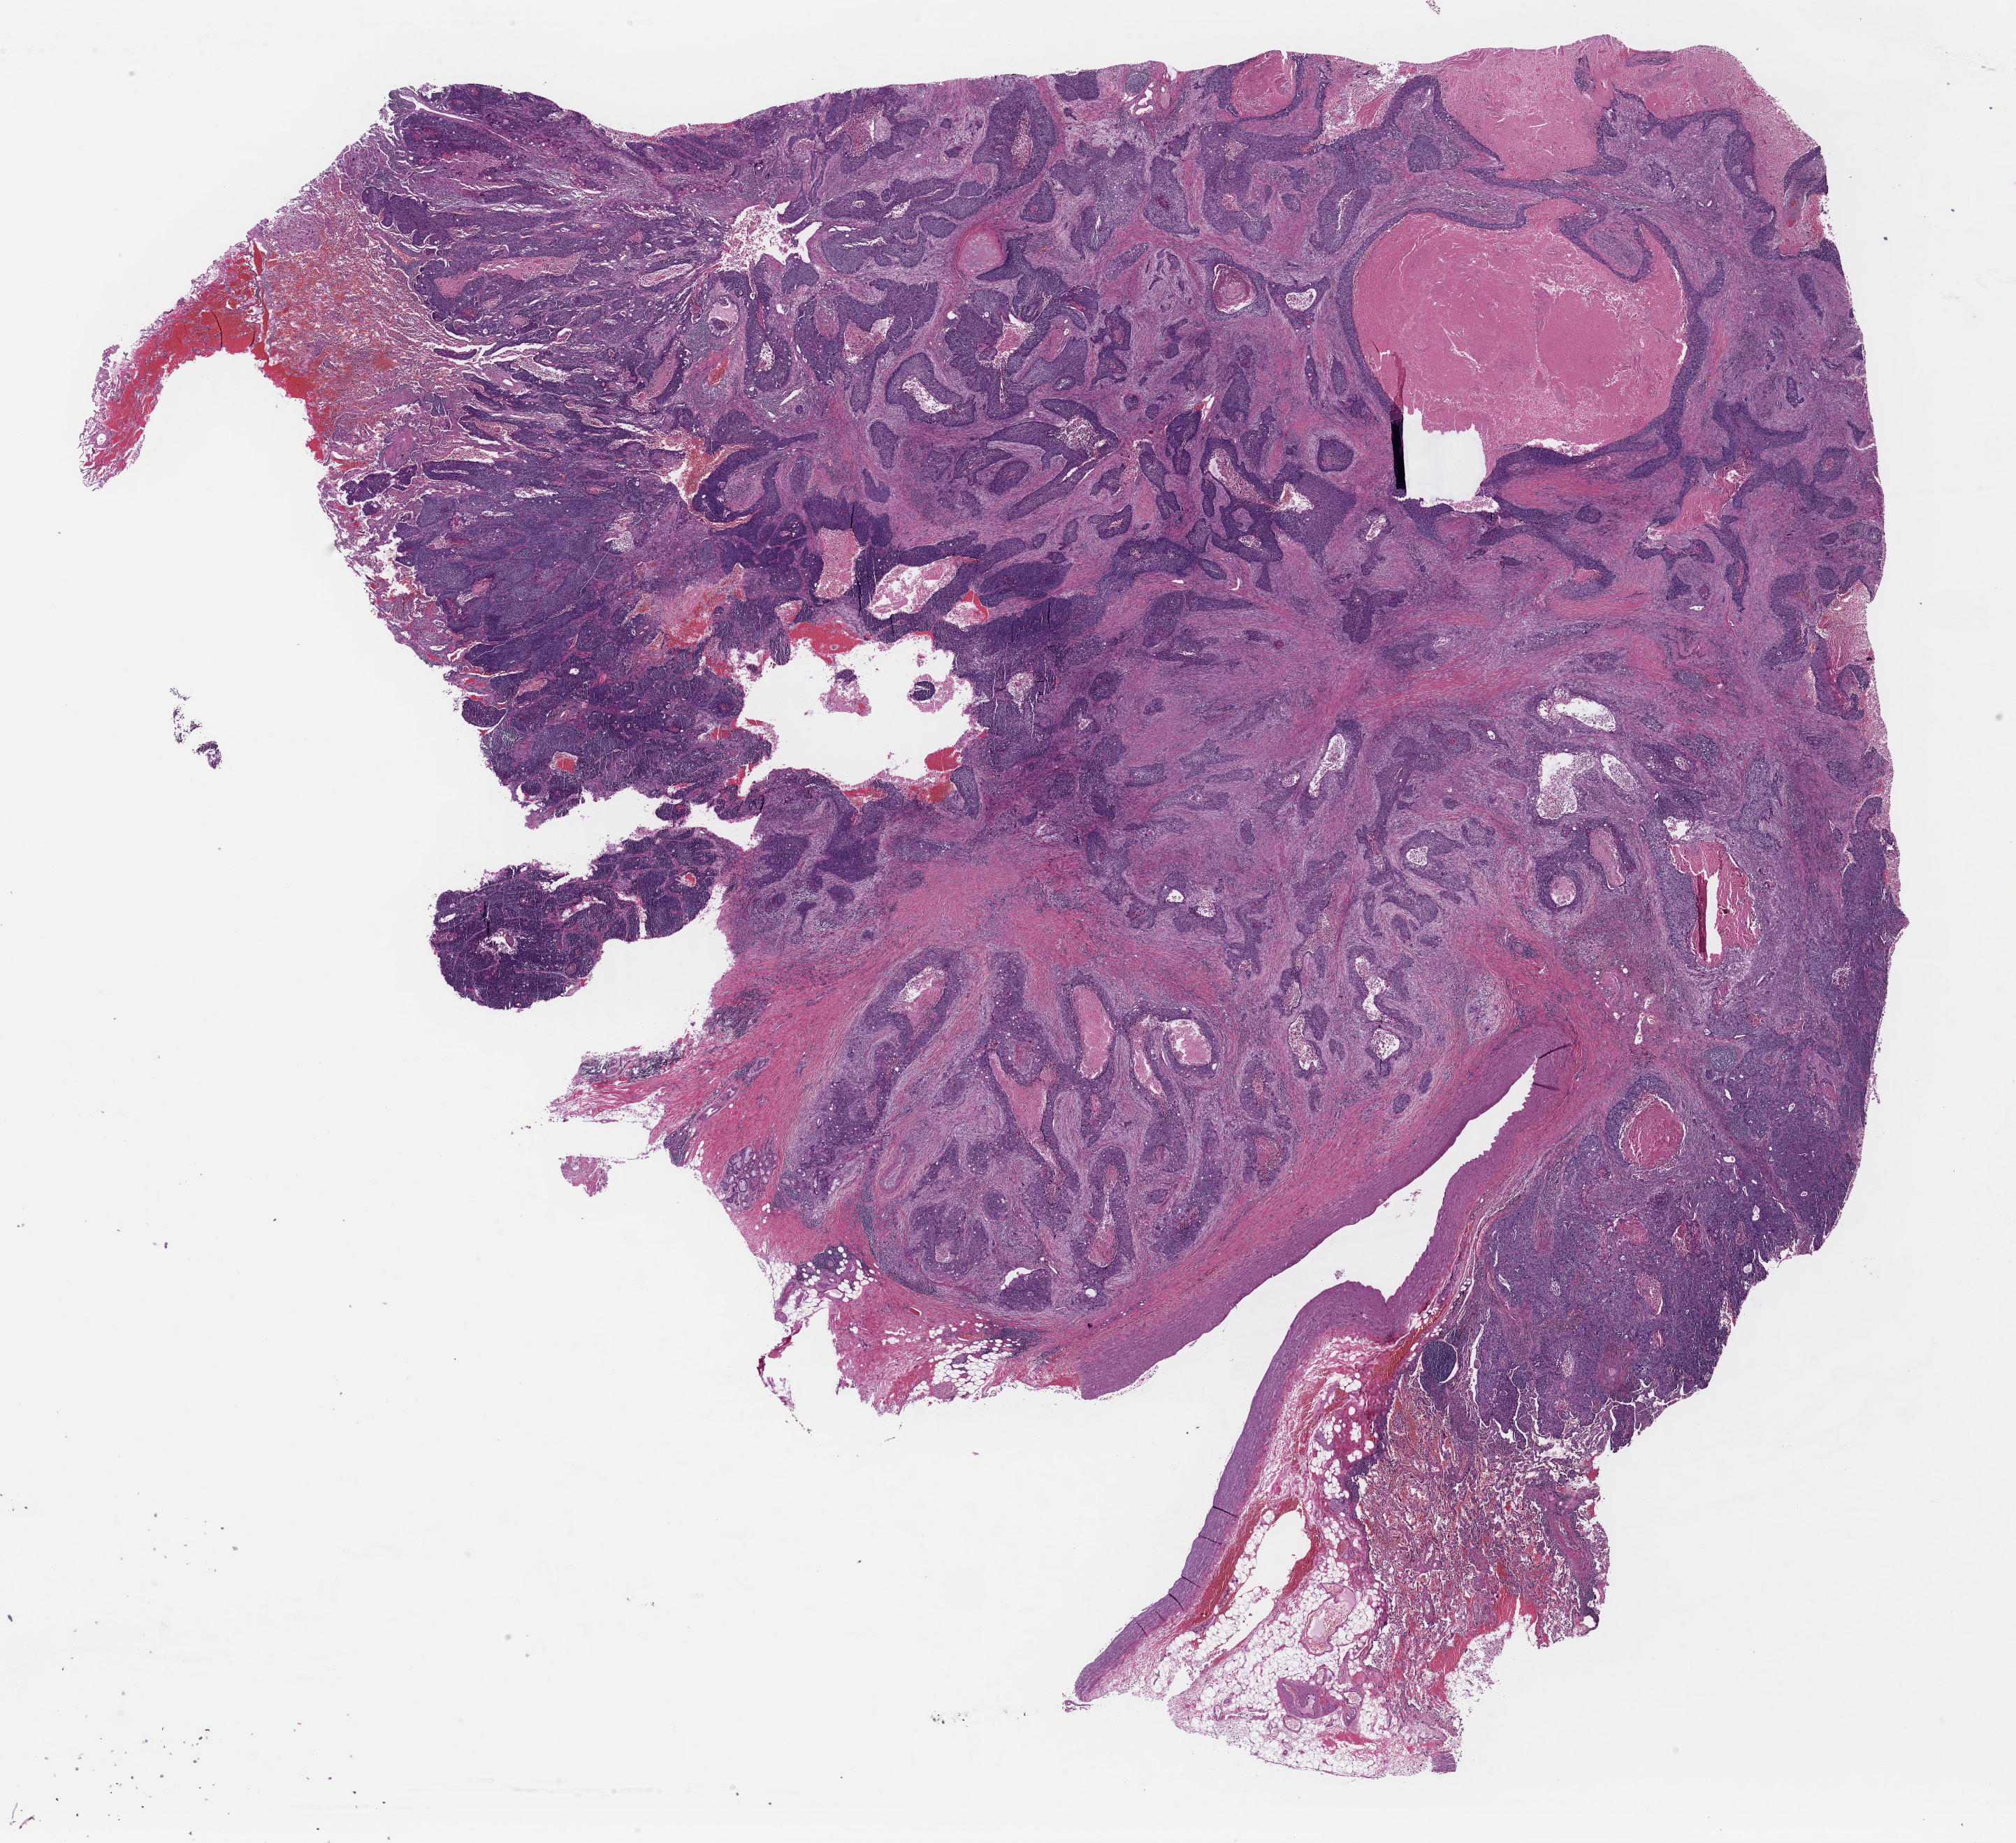
Hematoxylin and eosin (H&E) stained whole-slide image — whole scanned area (about 22.8 x 20.8 mm) shown as a low-resolution overview. FFPE section. Lung, primary tumour sample. Patient: male, age at initial diagnosis 68 years.
Pathologic diagnosis: Squamous cell carcinoma, NOS (lower lobe, lung).